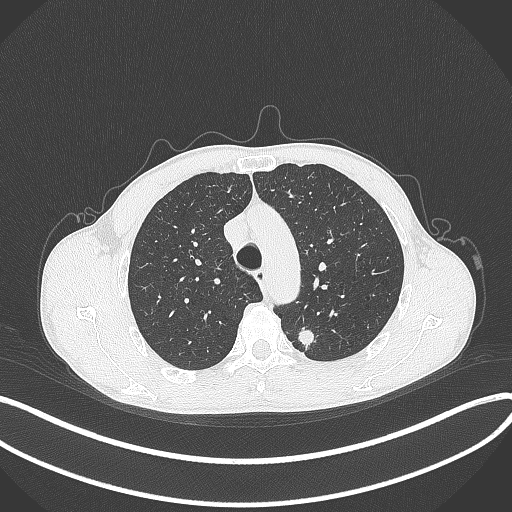
Chest CT, one axial slice; position 299 of 429 along the scan axis; 120 kVp; lung window (W 1500 / L -600 HU); 1 mm slice thickness; 512 × 512 image matrix, field of view 400 × 400 mm. Male patient, age 51 years. From the clinical record (not read from this slice): clinical TNM (as recorded): T2a N1 M1.
Annotated regions visible in this slice (rectangle marked by the reading radiologist):
- lung tumour (recorded histology: adenocarcinoma): bounding box (x1, y1, x2, y2) in pixels: (293, 323, 320, 353)